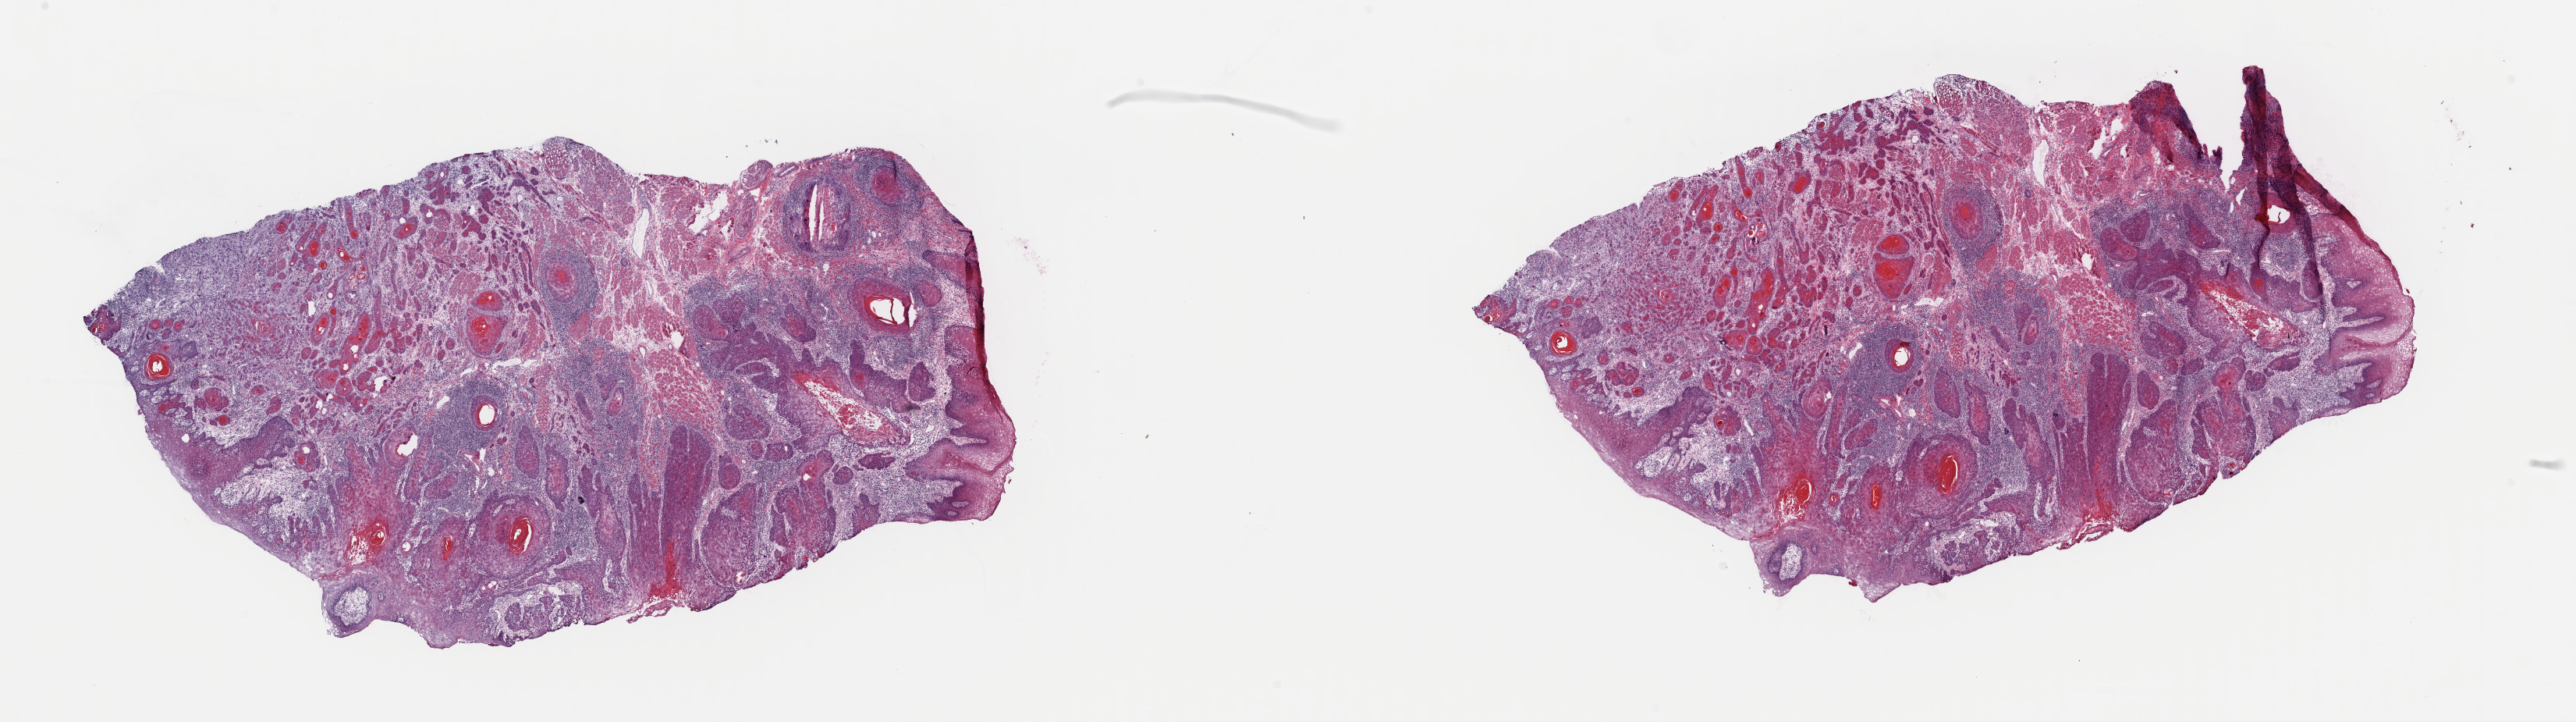
H&E whole-slide image, shown as a low-resolution overview of the whole scanned area (about 26.1 x 7.3 mm, acquisition: 40x scan); frozen section from the top of the tissue portion; head and neck, primary tumour sample. Female patient; age at initial diagnosis 24 years. Histologic grade: G1 (well differentiated). Pathologist review of this section (percent, as recorded): tumour cells 60%, tumour nuclei 60%, normal cells 10%, stromal cells 29%, necrosis 1%. Infiltration values recorded for this section: lymphocyte infiltration 6%, monocyte infiltration 2%, neutrophil infiltration 5%.
Lymph nodes positive (case pathology): 0 of 24 examined. Histologic diagnosis: Squamous cell carcinoma, keratinizing, NOS (tongue, NOS). AJCC pathologic stage: I (7th edition).